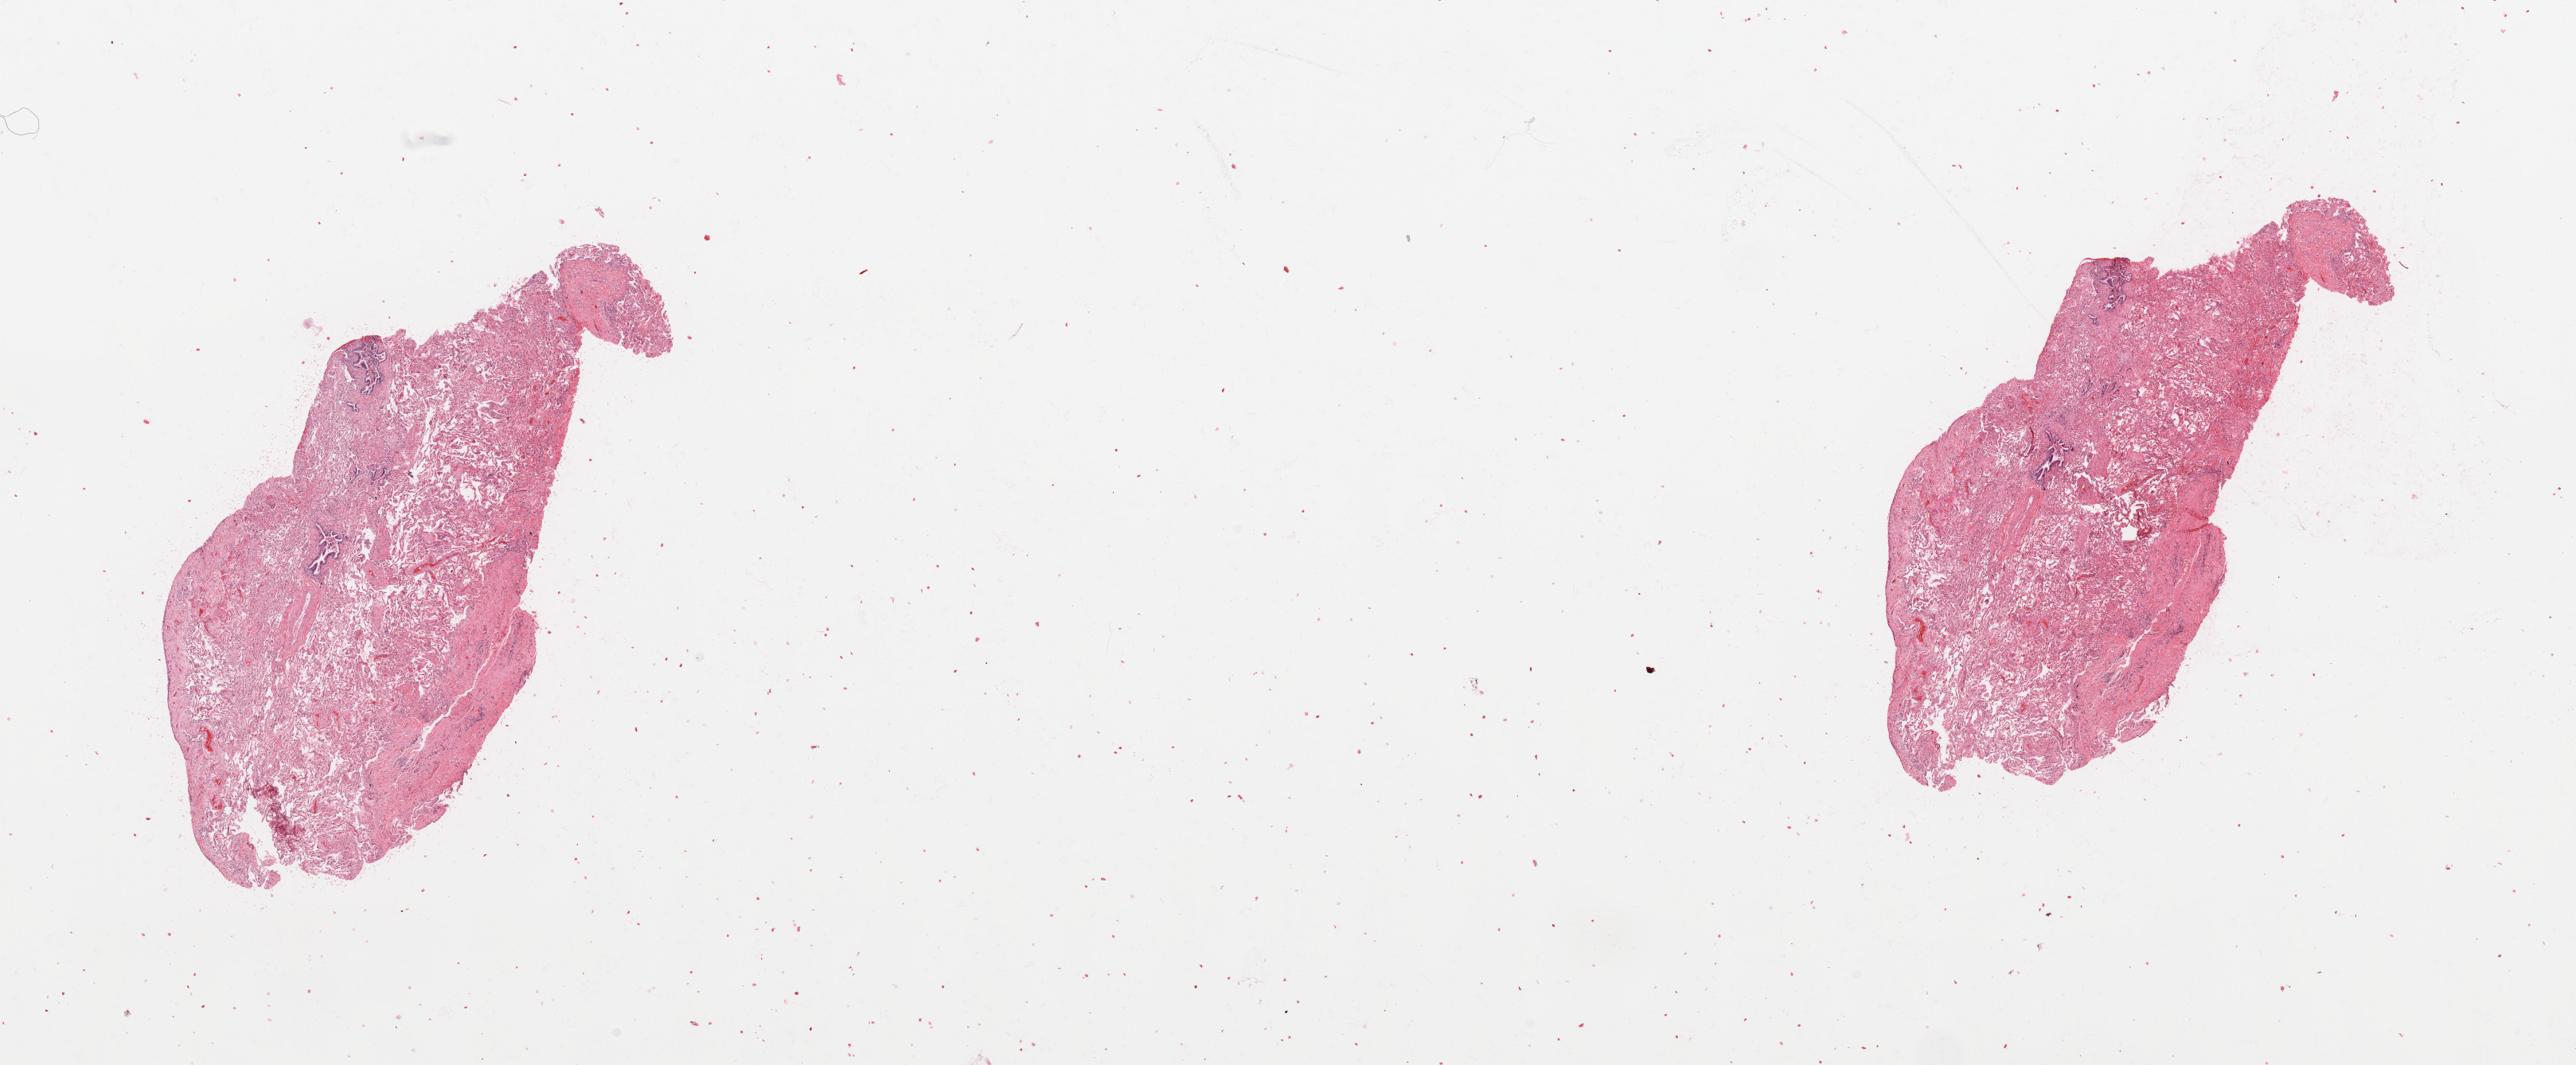
H&E whole-slide image, whole scanned area (about 25.6 x 10.6 mm, acquisition: 20x scan) shown as a low-resolution overview; normal (non-tumour) tissue sample, sampled site: lung. Male, 74 y/o.
- this section: normal (non-tumour) tissue from the same patient
- patient diagnosis: Squamous cell carcinoma, NOS